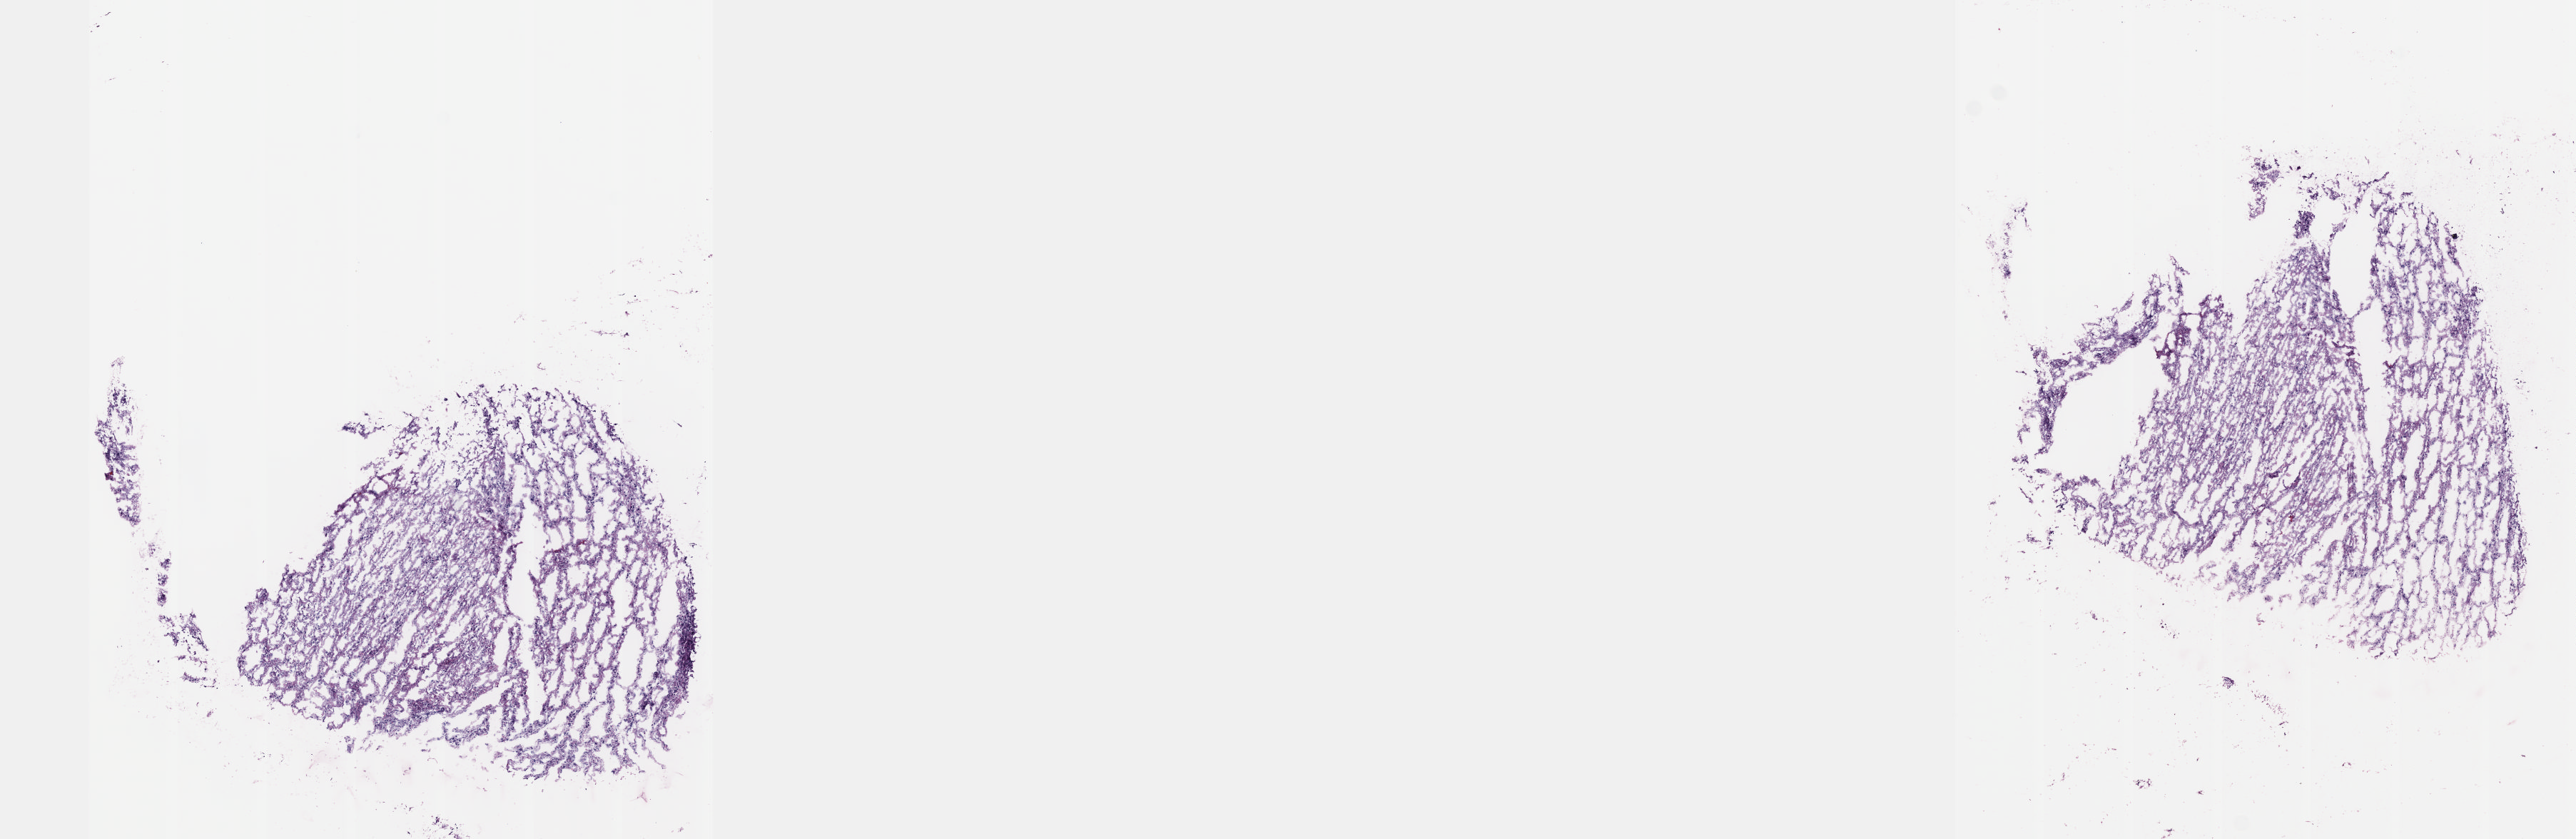
Digitized H&E tissue section (whole slide) — whole scanned area (about 14.6 x 4.8 mm, slide scanned at 40x) shown as a low-resolution overview, frozen section from the top of the tissue portion, primary tumour sample from the brain. Male patient; age at initial diagnosis 44 years. Histologic grade: G2 (moderately differentiated). Pathologist review of this section (percent, as recorded): tumour cells 35%, tumour nuclei 70%, normal cells 5%, stromal cells 60%, necrosis 0%. Inflammatory infiltration, as recorded: lymphocyte infiltration 0%, monocyte infiltration 0%, neutrophil infiltration 0%.
• histologic diagnosis: Astrocytoma, NOS
• laterality: left